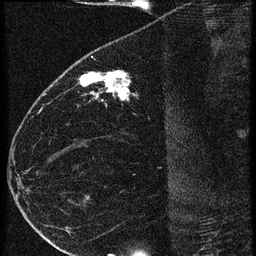
Breast MRI (dynamic contrast-enhanced), one sagittal slice. Slice 26 of 60 in the series (ordered by position). 3 images stored at this slice position (order not interpretable as contrast timing). 1.5 T. TE 4.2 ms, TR 20.4 ms. 1.5 mm slice thickness. 256 × 256 image matrix, field of view 180 × 180 mm. Female patient, age 35 years. From the clinical record (not read from this slice): setting: breast cancer imaged before/during neoadjuvant chemotherapy; receptor status: HR-positive, HER2-negative.
Structures marked on this image (semi-automatically segmented with operator editing):
- analysis volume of interest (the breast-tissue region the enhancement analysis was run in; not a lesion): bounding box (x1, y1, x2, y2) in pixels: (65, 60, 169, 119)
- tumour enhancement mask (voxels above the 90 % enhancement threshold inside the analysis volume of interest): (79, 70, 130, 101)